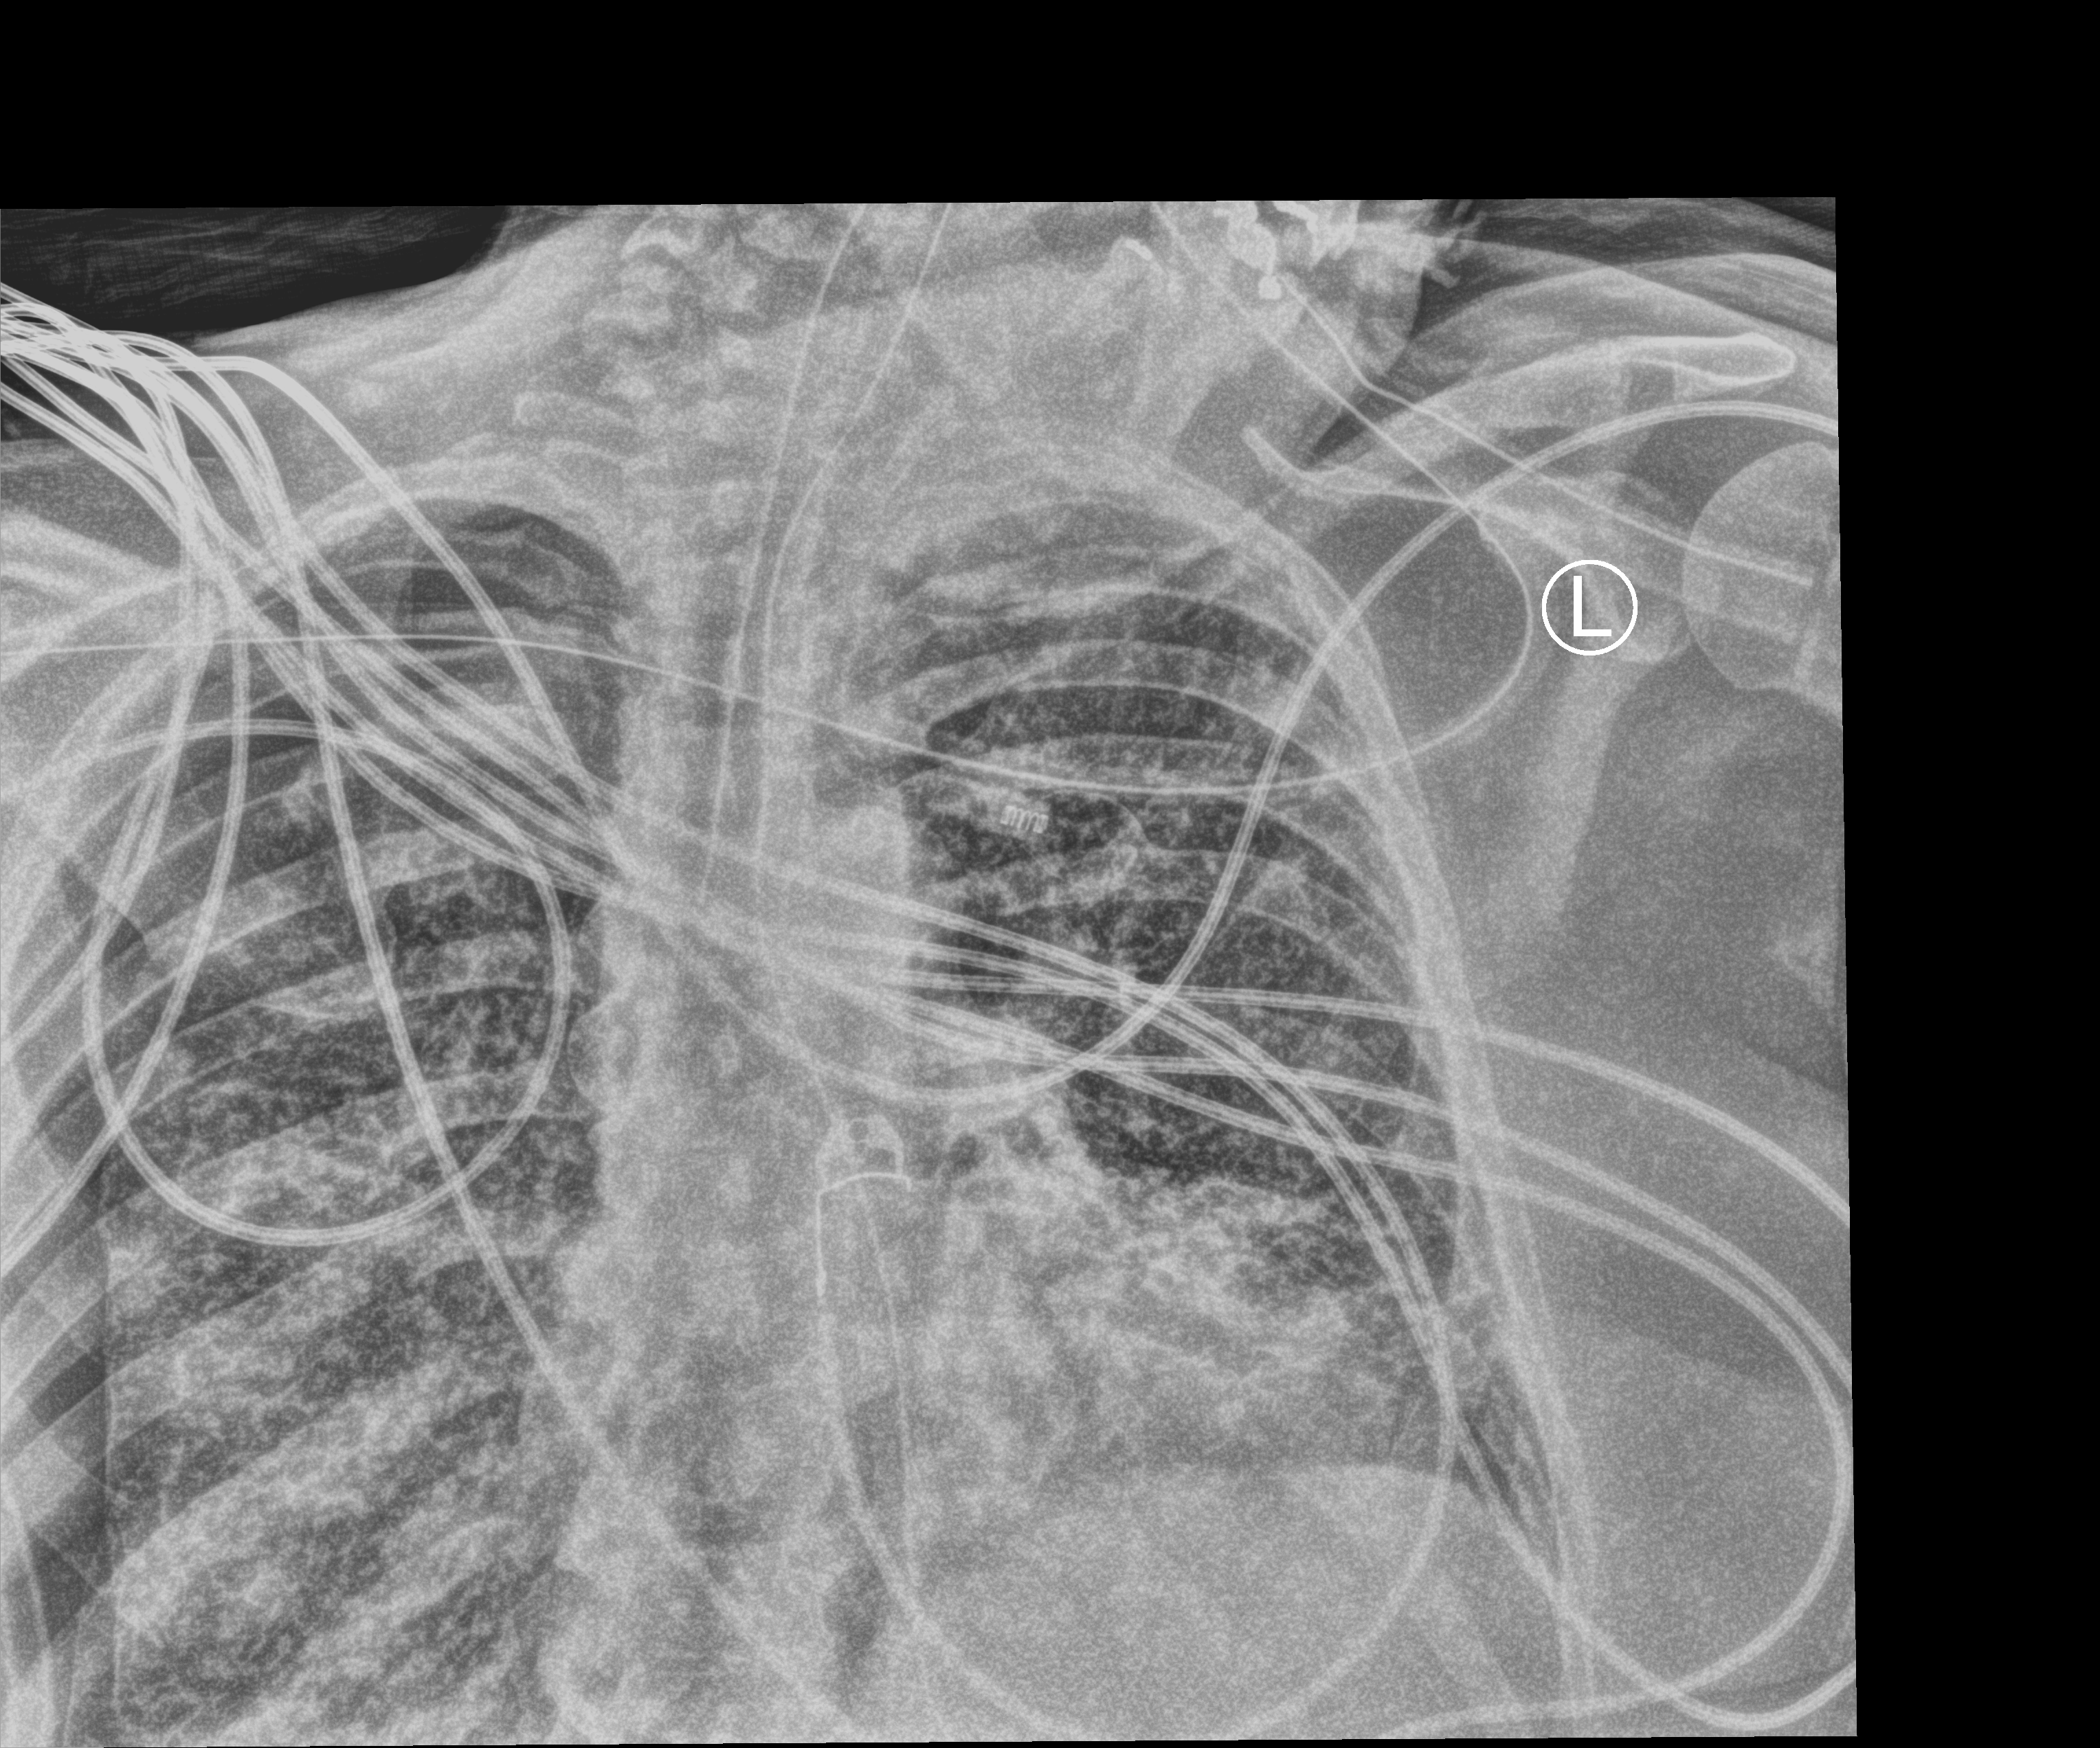
Chest X-ray (portable); anteroposterior (AP) projection. Patient hospitalised with COVID-19, aged 18–59 years.
Hospital-stay facts (about this admission, not read from this image; timing relative to this image not recorded): mechanically ventilated during this hospital stay: yes; admitted to intensive care during this hospital stay: yes.